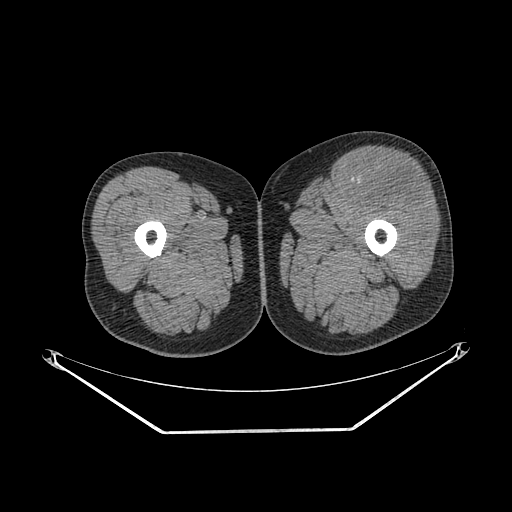
CT of an extremity soft-tissue mass (from a PET/CT study), one axial slice. Position 235 of 267 along the scan axis. 140 kVp. Soft-tissue window (W 400 / L 40 HU). 3.75 mm slice thickness. 512 × 512 image matrix. Male patient. Case-level facts recorded for this patient, not image findings: histological type: extraskeletal osteosarcoma; grade: high; site of the primary tumour: thigh.
Structures marked on this image (expert contour drawn on MRI and transferred to this co-registered scan by the dataset authors):
- gross tumour volume (mass): box from (x=352, y=160) to (x=428, y=211) px